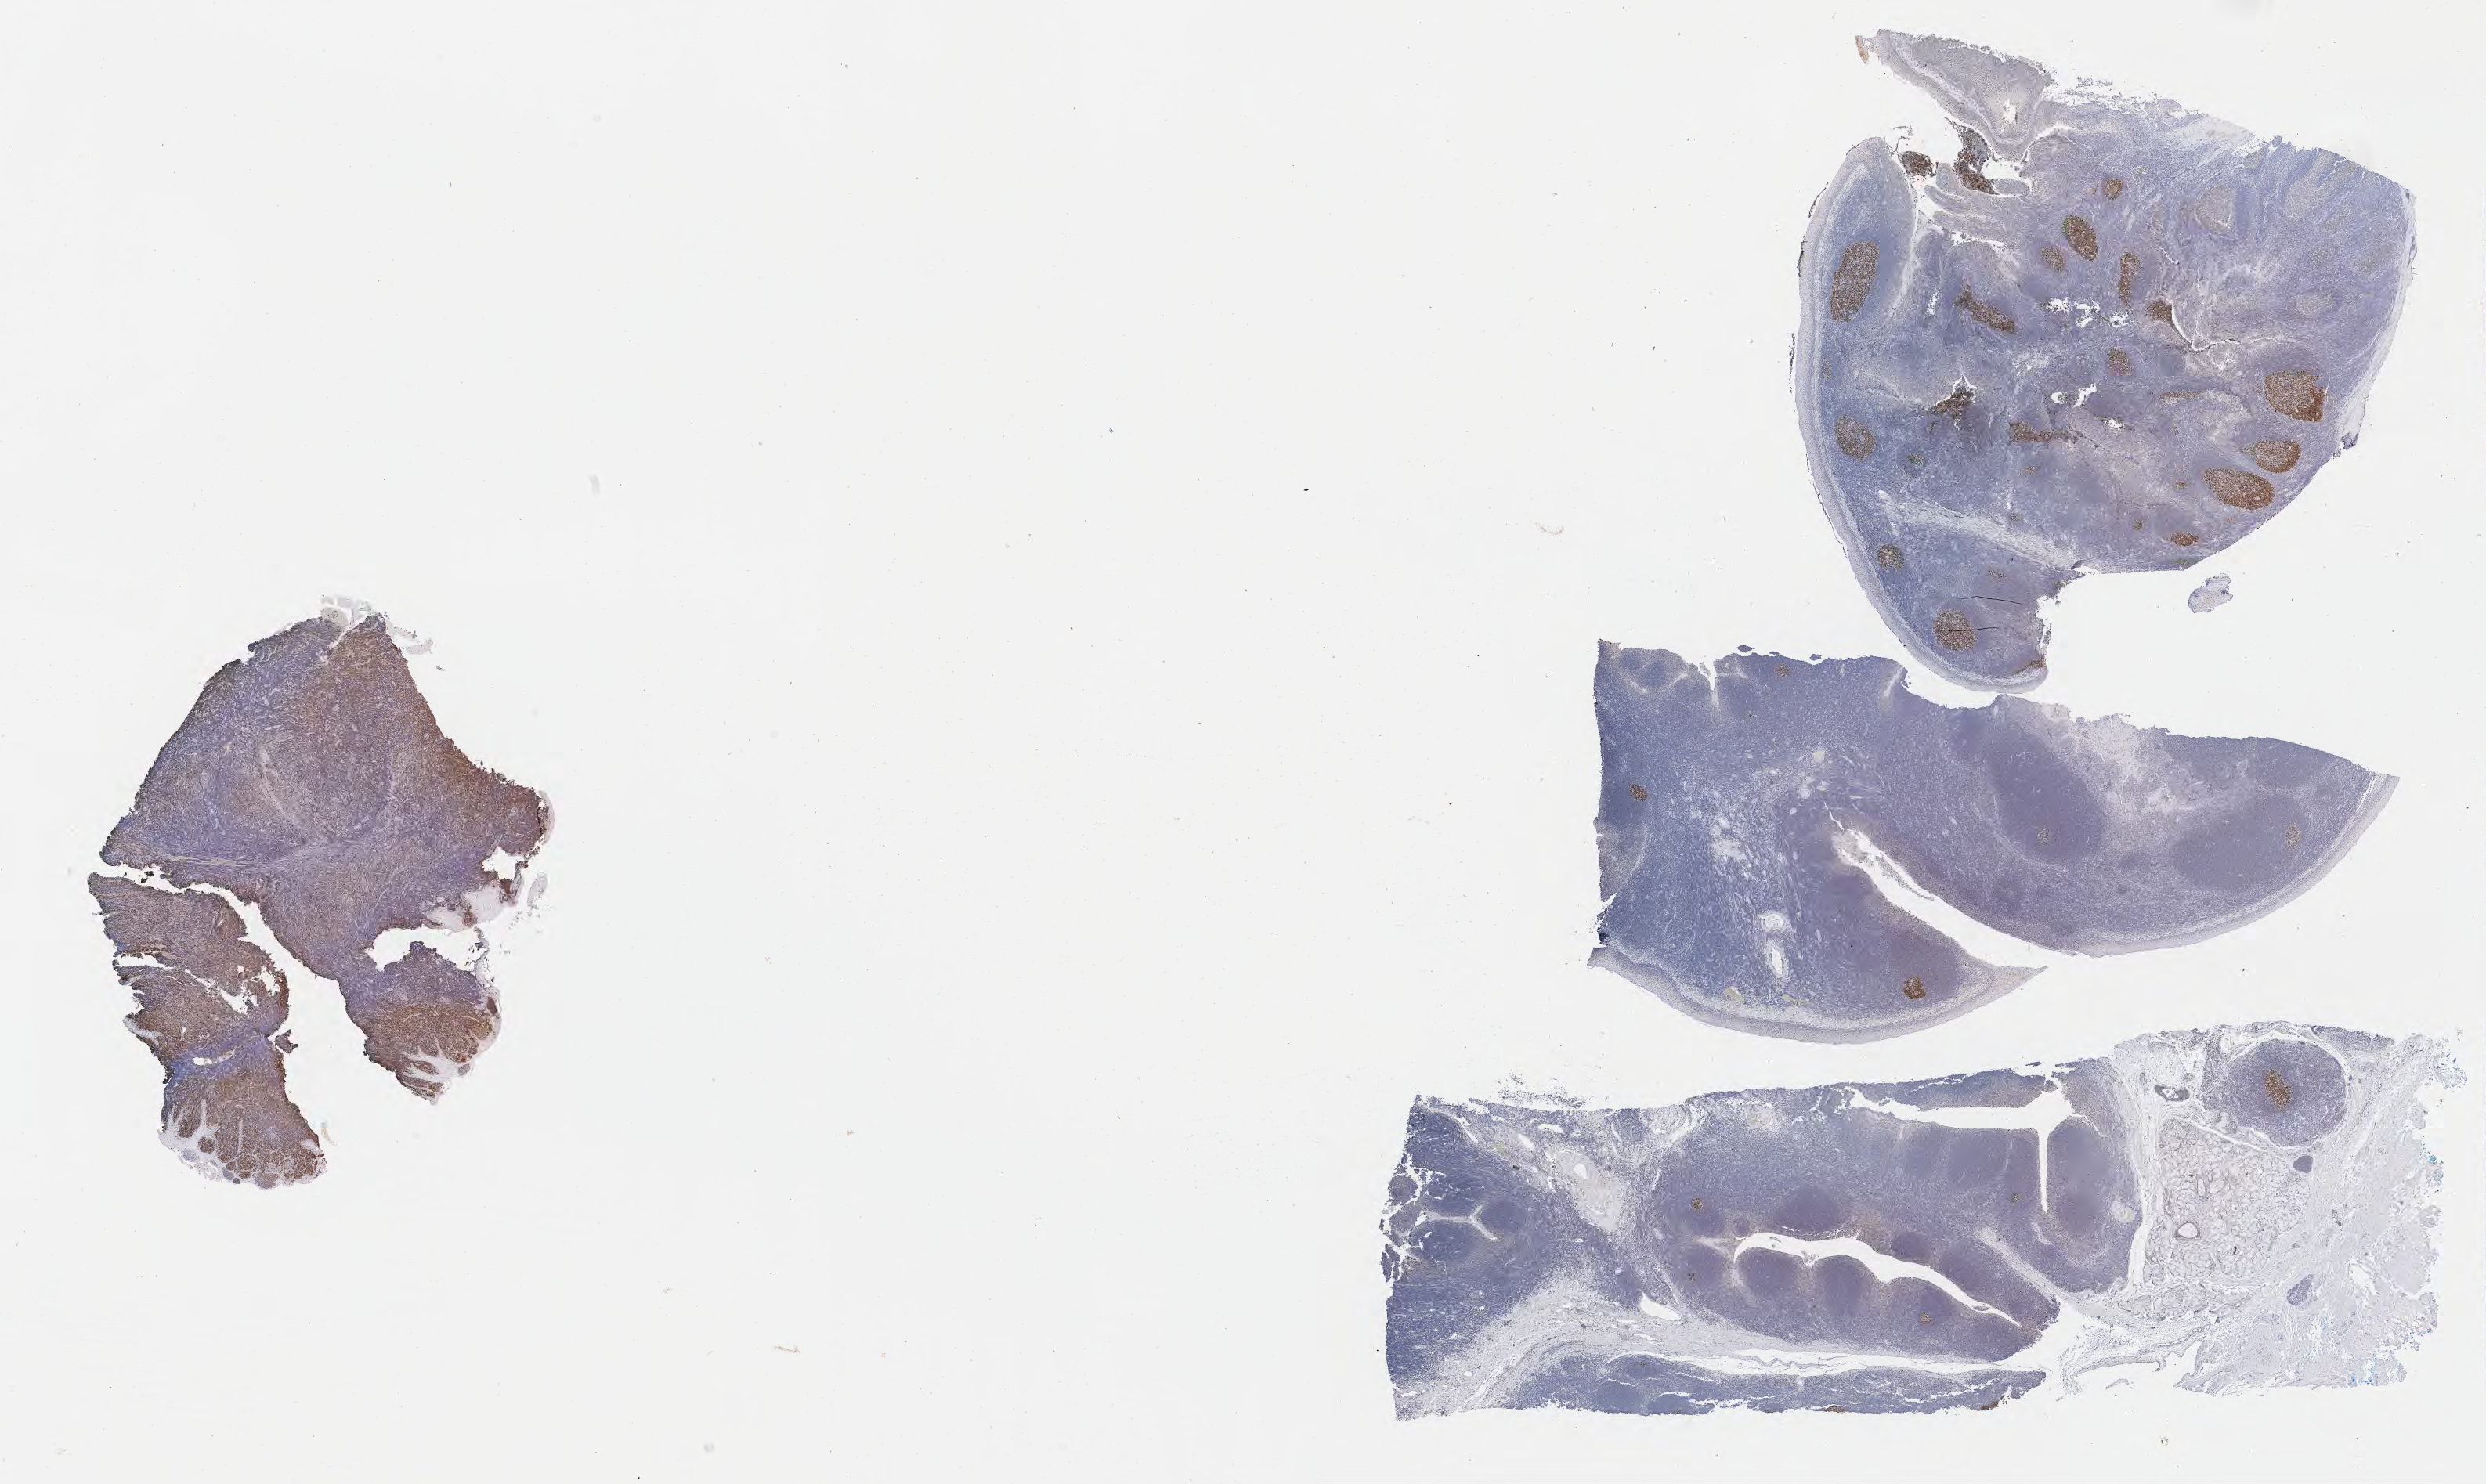
Immunohistochemistry (IHC) whole-slide image stained for BCL6, whole scanned area (about 25.7 x 15.3 mm) shown as a low-resolution overview; specimen: tumor tissue; anatomic site: cranium. Patient male; aged 11.
Histologic diagnosis: Diffuse large B-cell lymphoma, NOS.